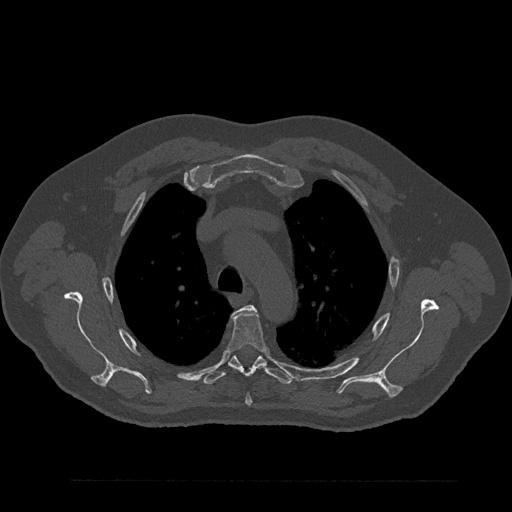
CT including the spine, one axial slice. Position 629 of 797 along the scan axis. 120 kVp. Bone window (W 1800 / L 400 HU). 512 × 512 image matrix. Patient: male, 61 years. Case-level facts recorded for this patient, not image findings: primary cancer: prostate.
Annotated regions visible in this slice (semi-automatic segmentation, software-assisted and operator-edited):
- T3 vertebra: box from (x=243, y=305) to (x=256, y=310) px
- T4 vertebra: (x=227, y=309)–(x=267, y=406)
- T5 vertebra: (x=203, y=356)–(x=292, y=386)